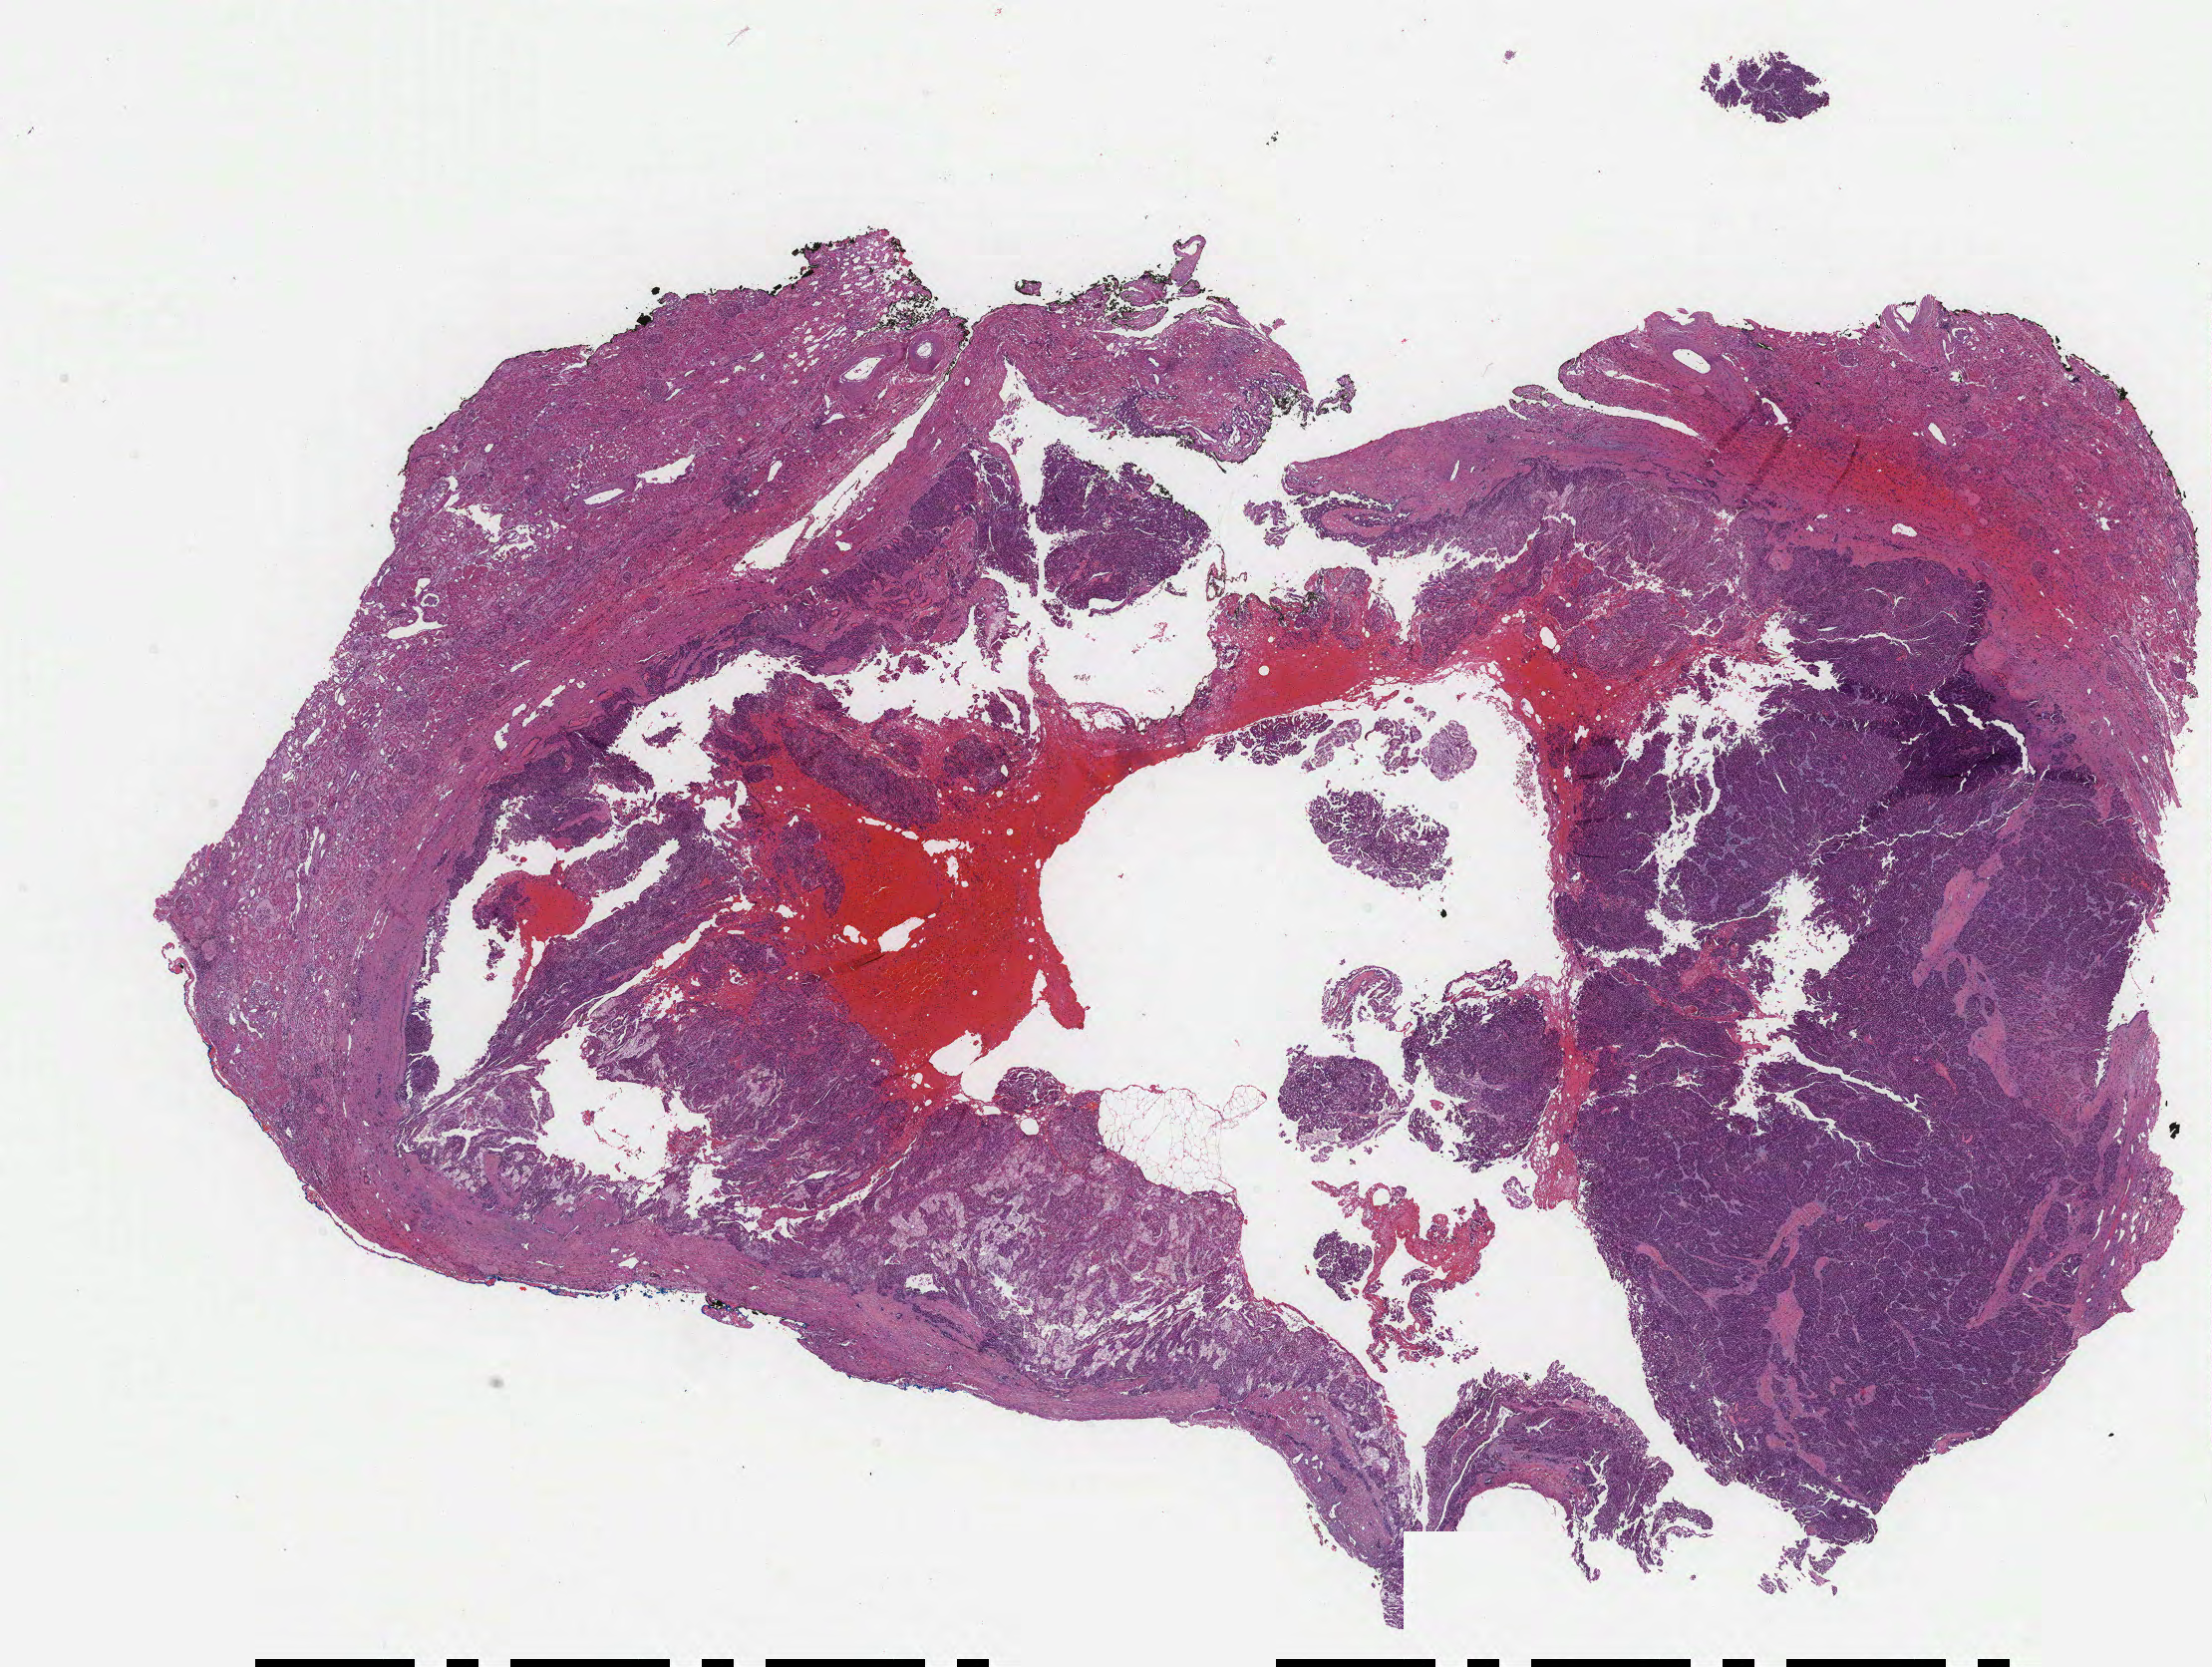
Digitized Hematoxylin and eosin (H&E) stained tissue section (whole slide), shown as a low-resolution overview of the whole scanned area (about 17.9 x 13.5 mm, acquisition: 40x scan); formalin-fixed paraffin-embedded (FFPE) diagnostic section; sample: primary tumour, kidney. Male, age 74 years at initial diagnosis.
• AJCC pathologic stage: I (7th edition)
• diagnosis: Papillary adenocarcinoma, NOS